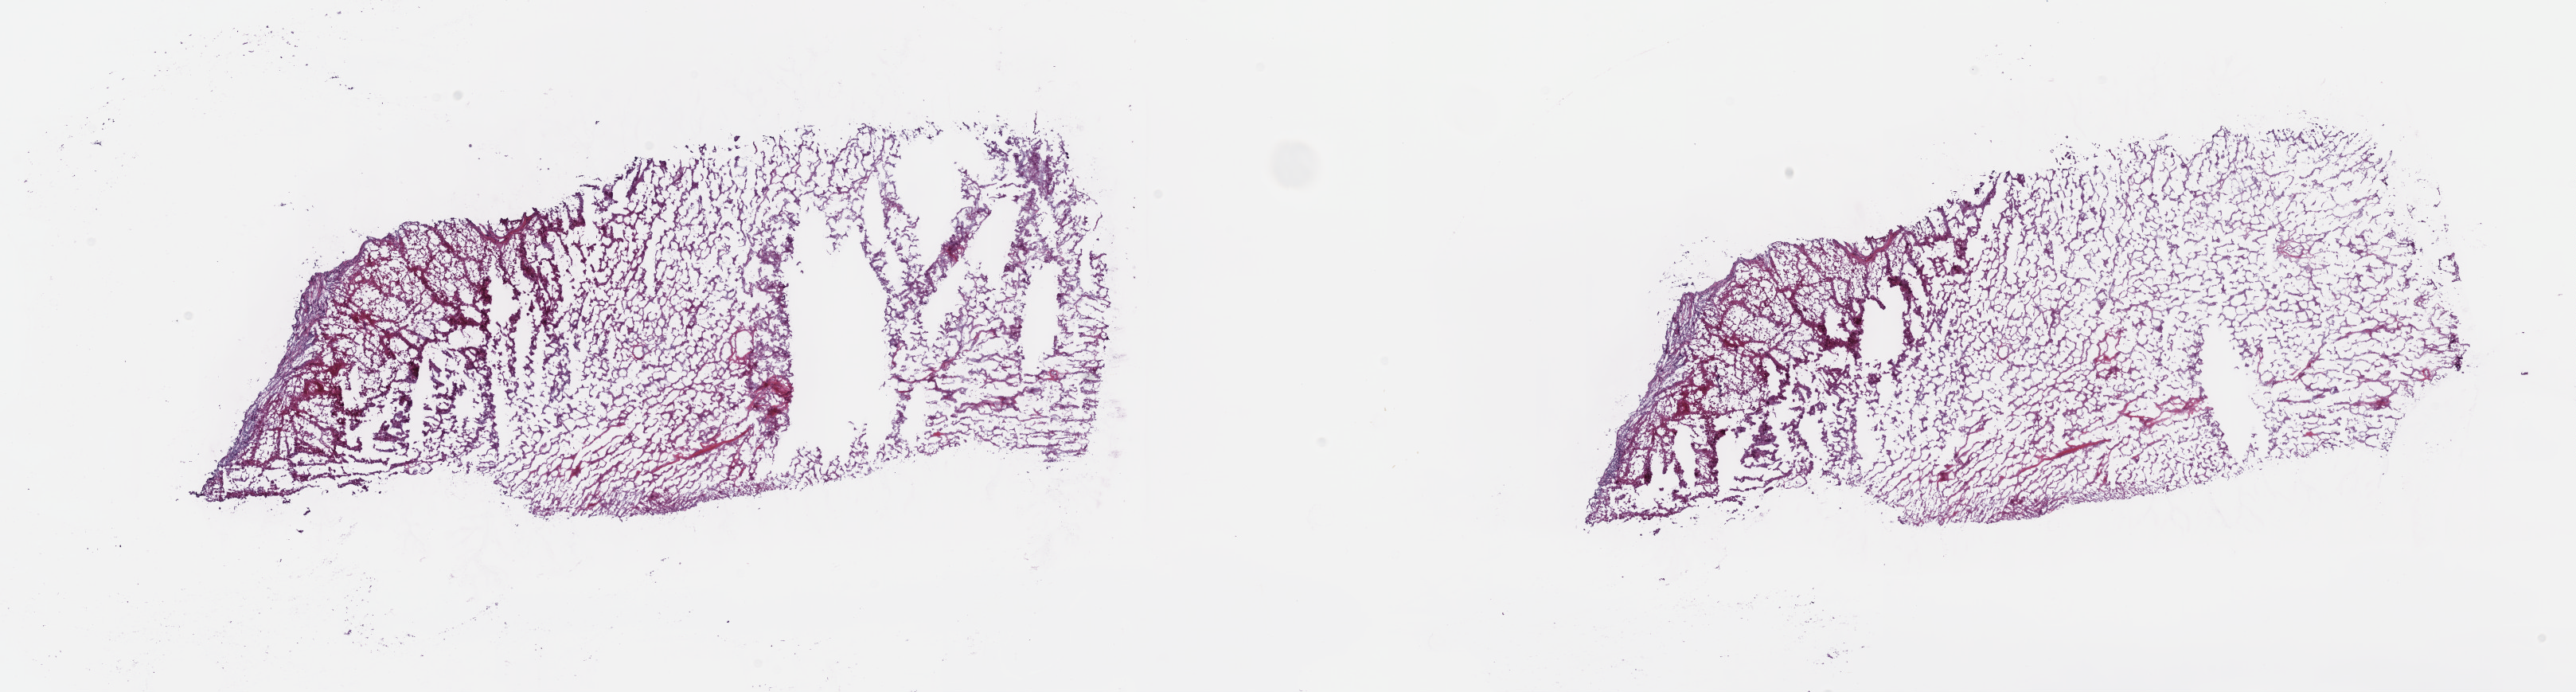
Digitized H&E-stained tissue section (whole slide) — whole scanned area (about 26.2 x 7.0 mm) shown as a low-resolution overview, frozen section from the top of the tissue portion, testis, primary tumour sample. Male, age 31 years at initial diagnosis. Composition of this section per pathologist review: tumour cells 0%, tumour nuclei 75%, normal cells 0%, stromal cells 10%, necrosis 90%. Infiltration values recorded for this section: lymphocyte infiltration 0%, monocyte infiltration 0%, neutrophil infiltration 0%.
Laterality: right. TNM: T1 N0 M0. Histologic diagnosis: Seminoma, NOS. AJCC pathologic stage: IA (7th edition).